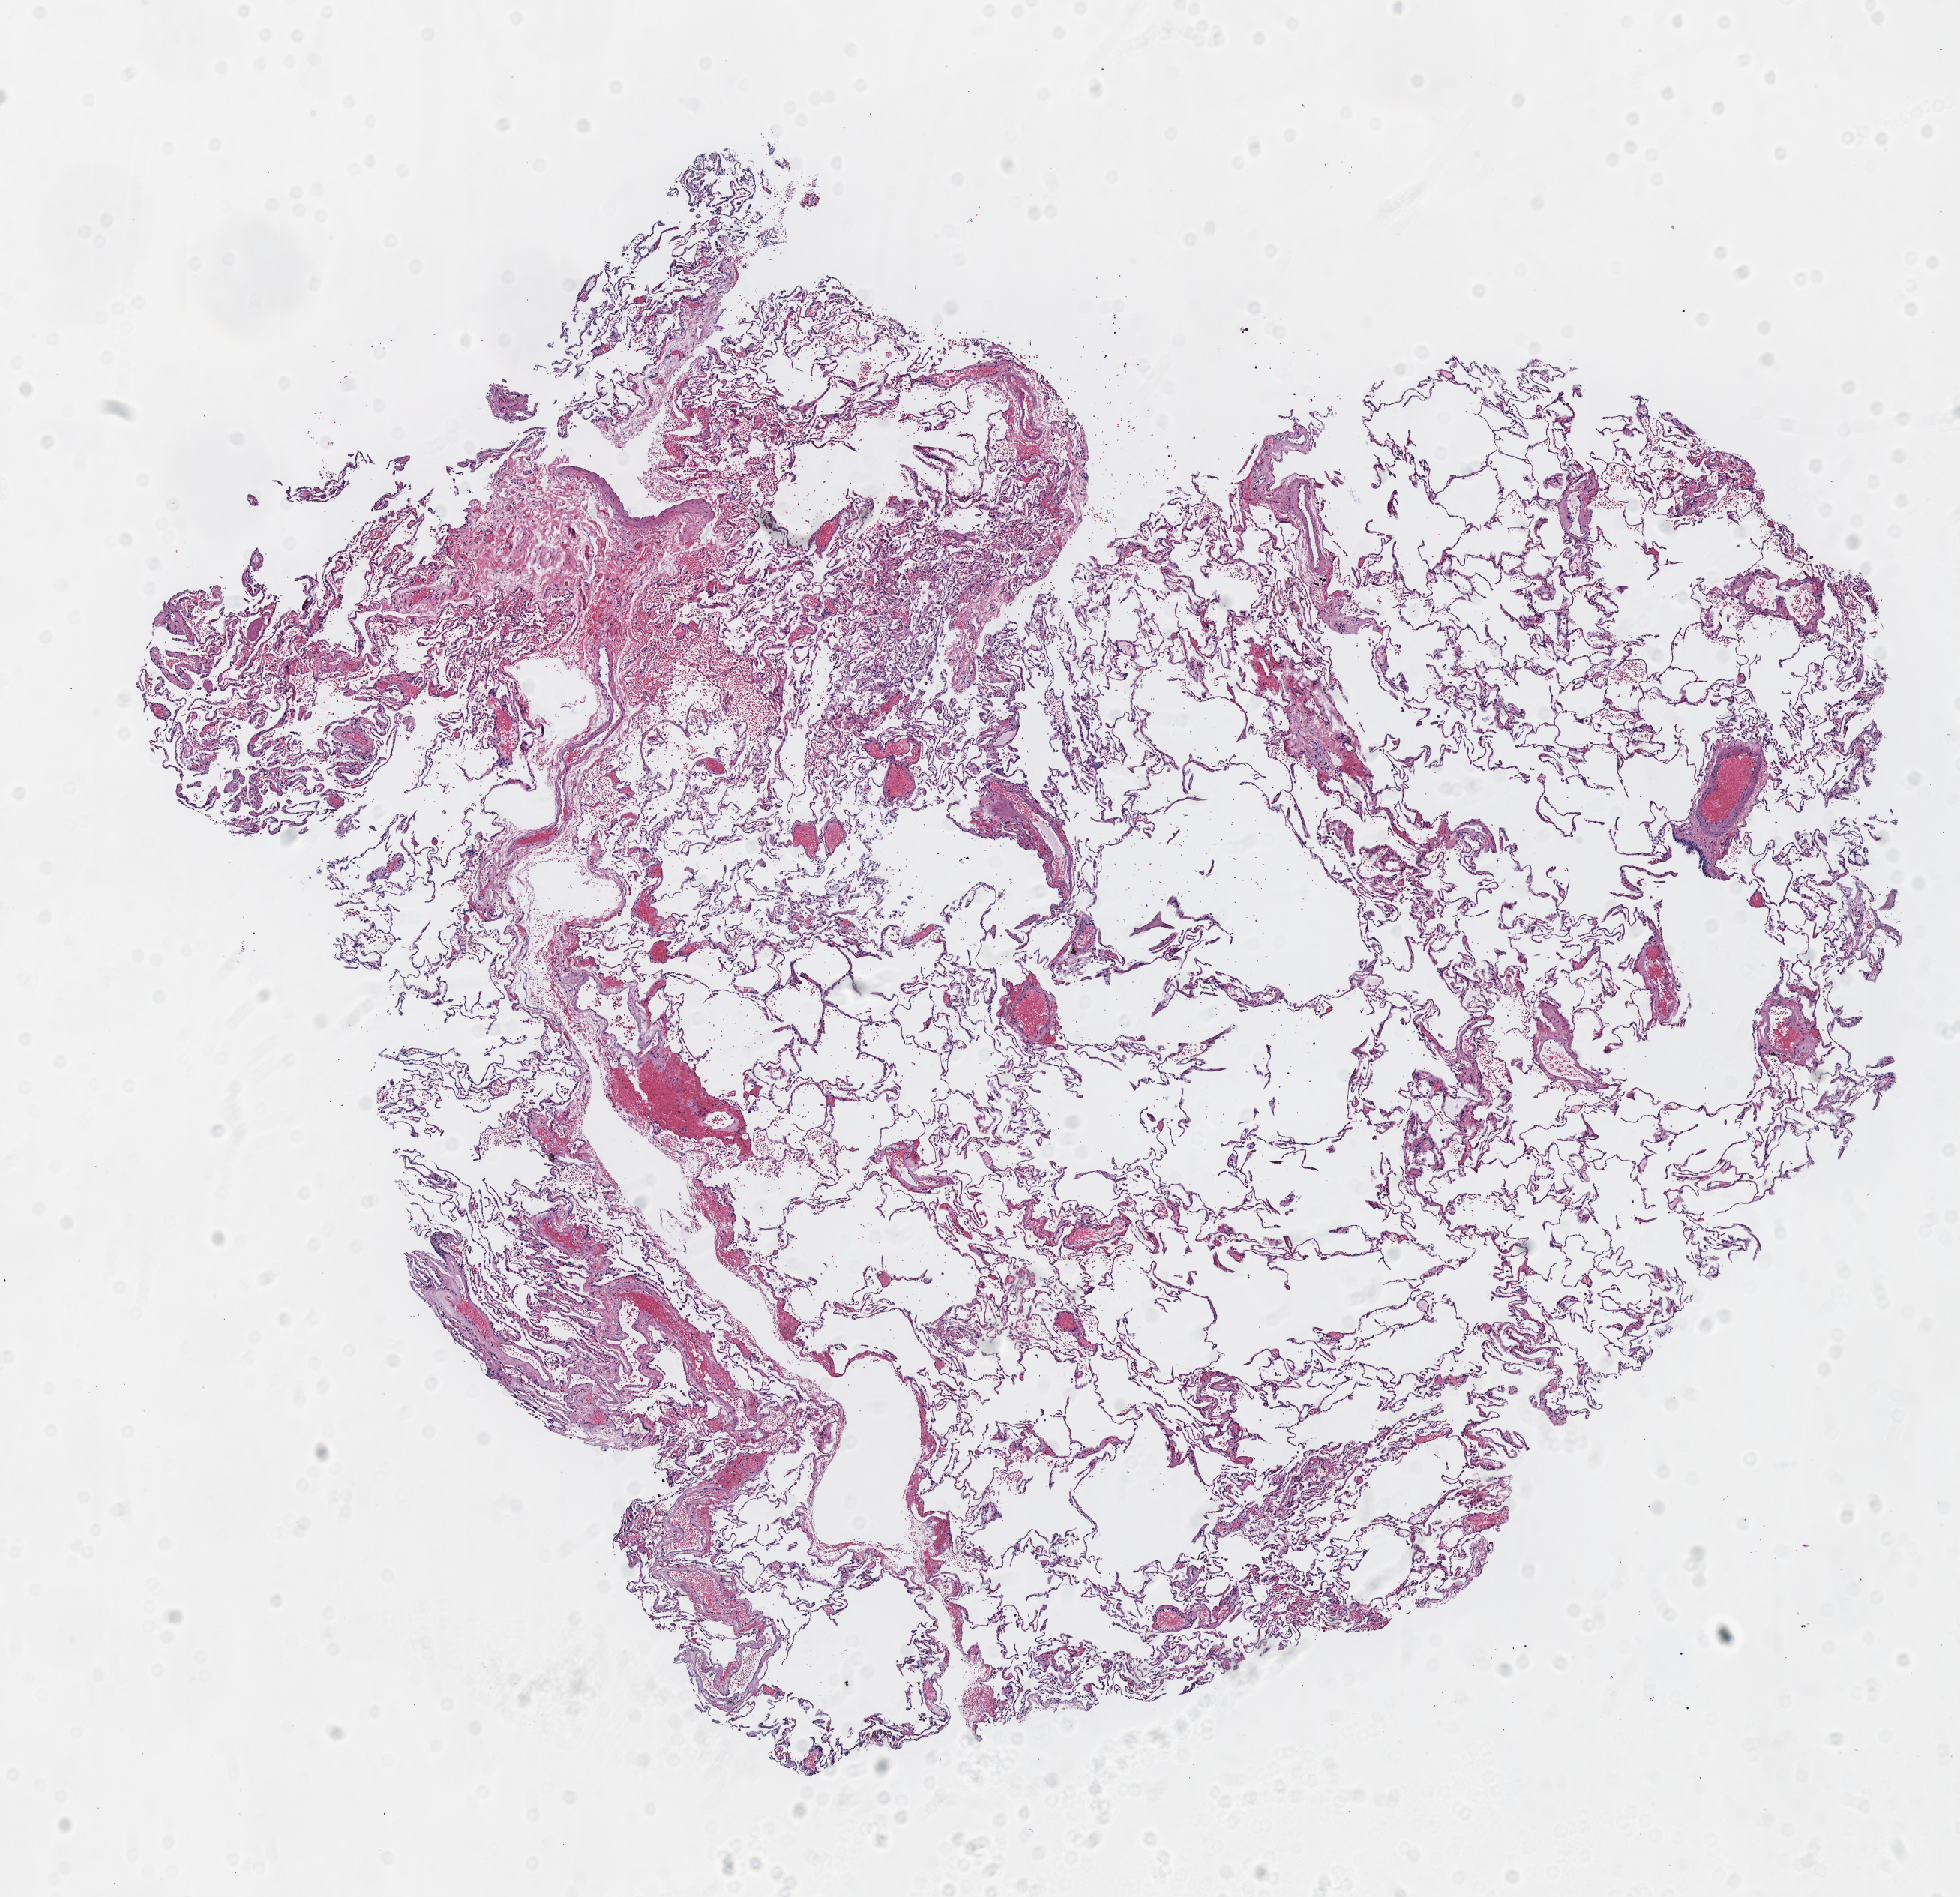
Digitized H&E-stained tissue section (whole slide) — whole scanned area (about 10.3 x 9.9 mm) shown as a low-resolution overview. Frozen section from the top of the tissue portion. Solid tissue normal (non-tumour tissue) sample from the lung. Male, age 61 years at initial diagnosis.
This section: solid tissue normal sample (biorepository sample class). Patient diagnosis: Adenocarcinoma, NOS.